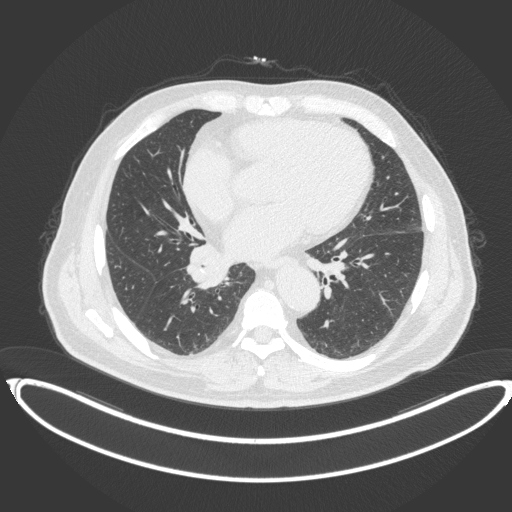
Chest CT, one axial slice. Position 182 of 383 along the scan axis. Reconstruction kernel B31f. Lung window (W 1500 / L -600 HU). 1 mm slice thickness. 512 × 512 image matrix. Patient: male, 61 years. From the clinical record (not read from this slice): clinical TNM (as recorded): T1b N1 M0.
Outlined on this slice (rectangle marked by the reading radiologist):
- lung tumour (recorded histology: squamous cell carcinoma): bounding box <187,242,231,291> (left, top, right, bottom; pixels)